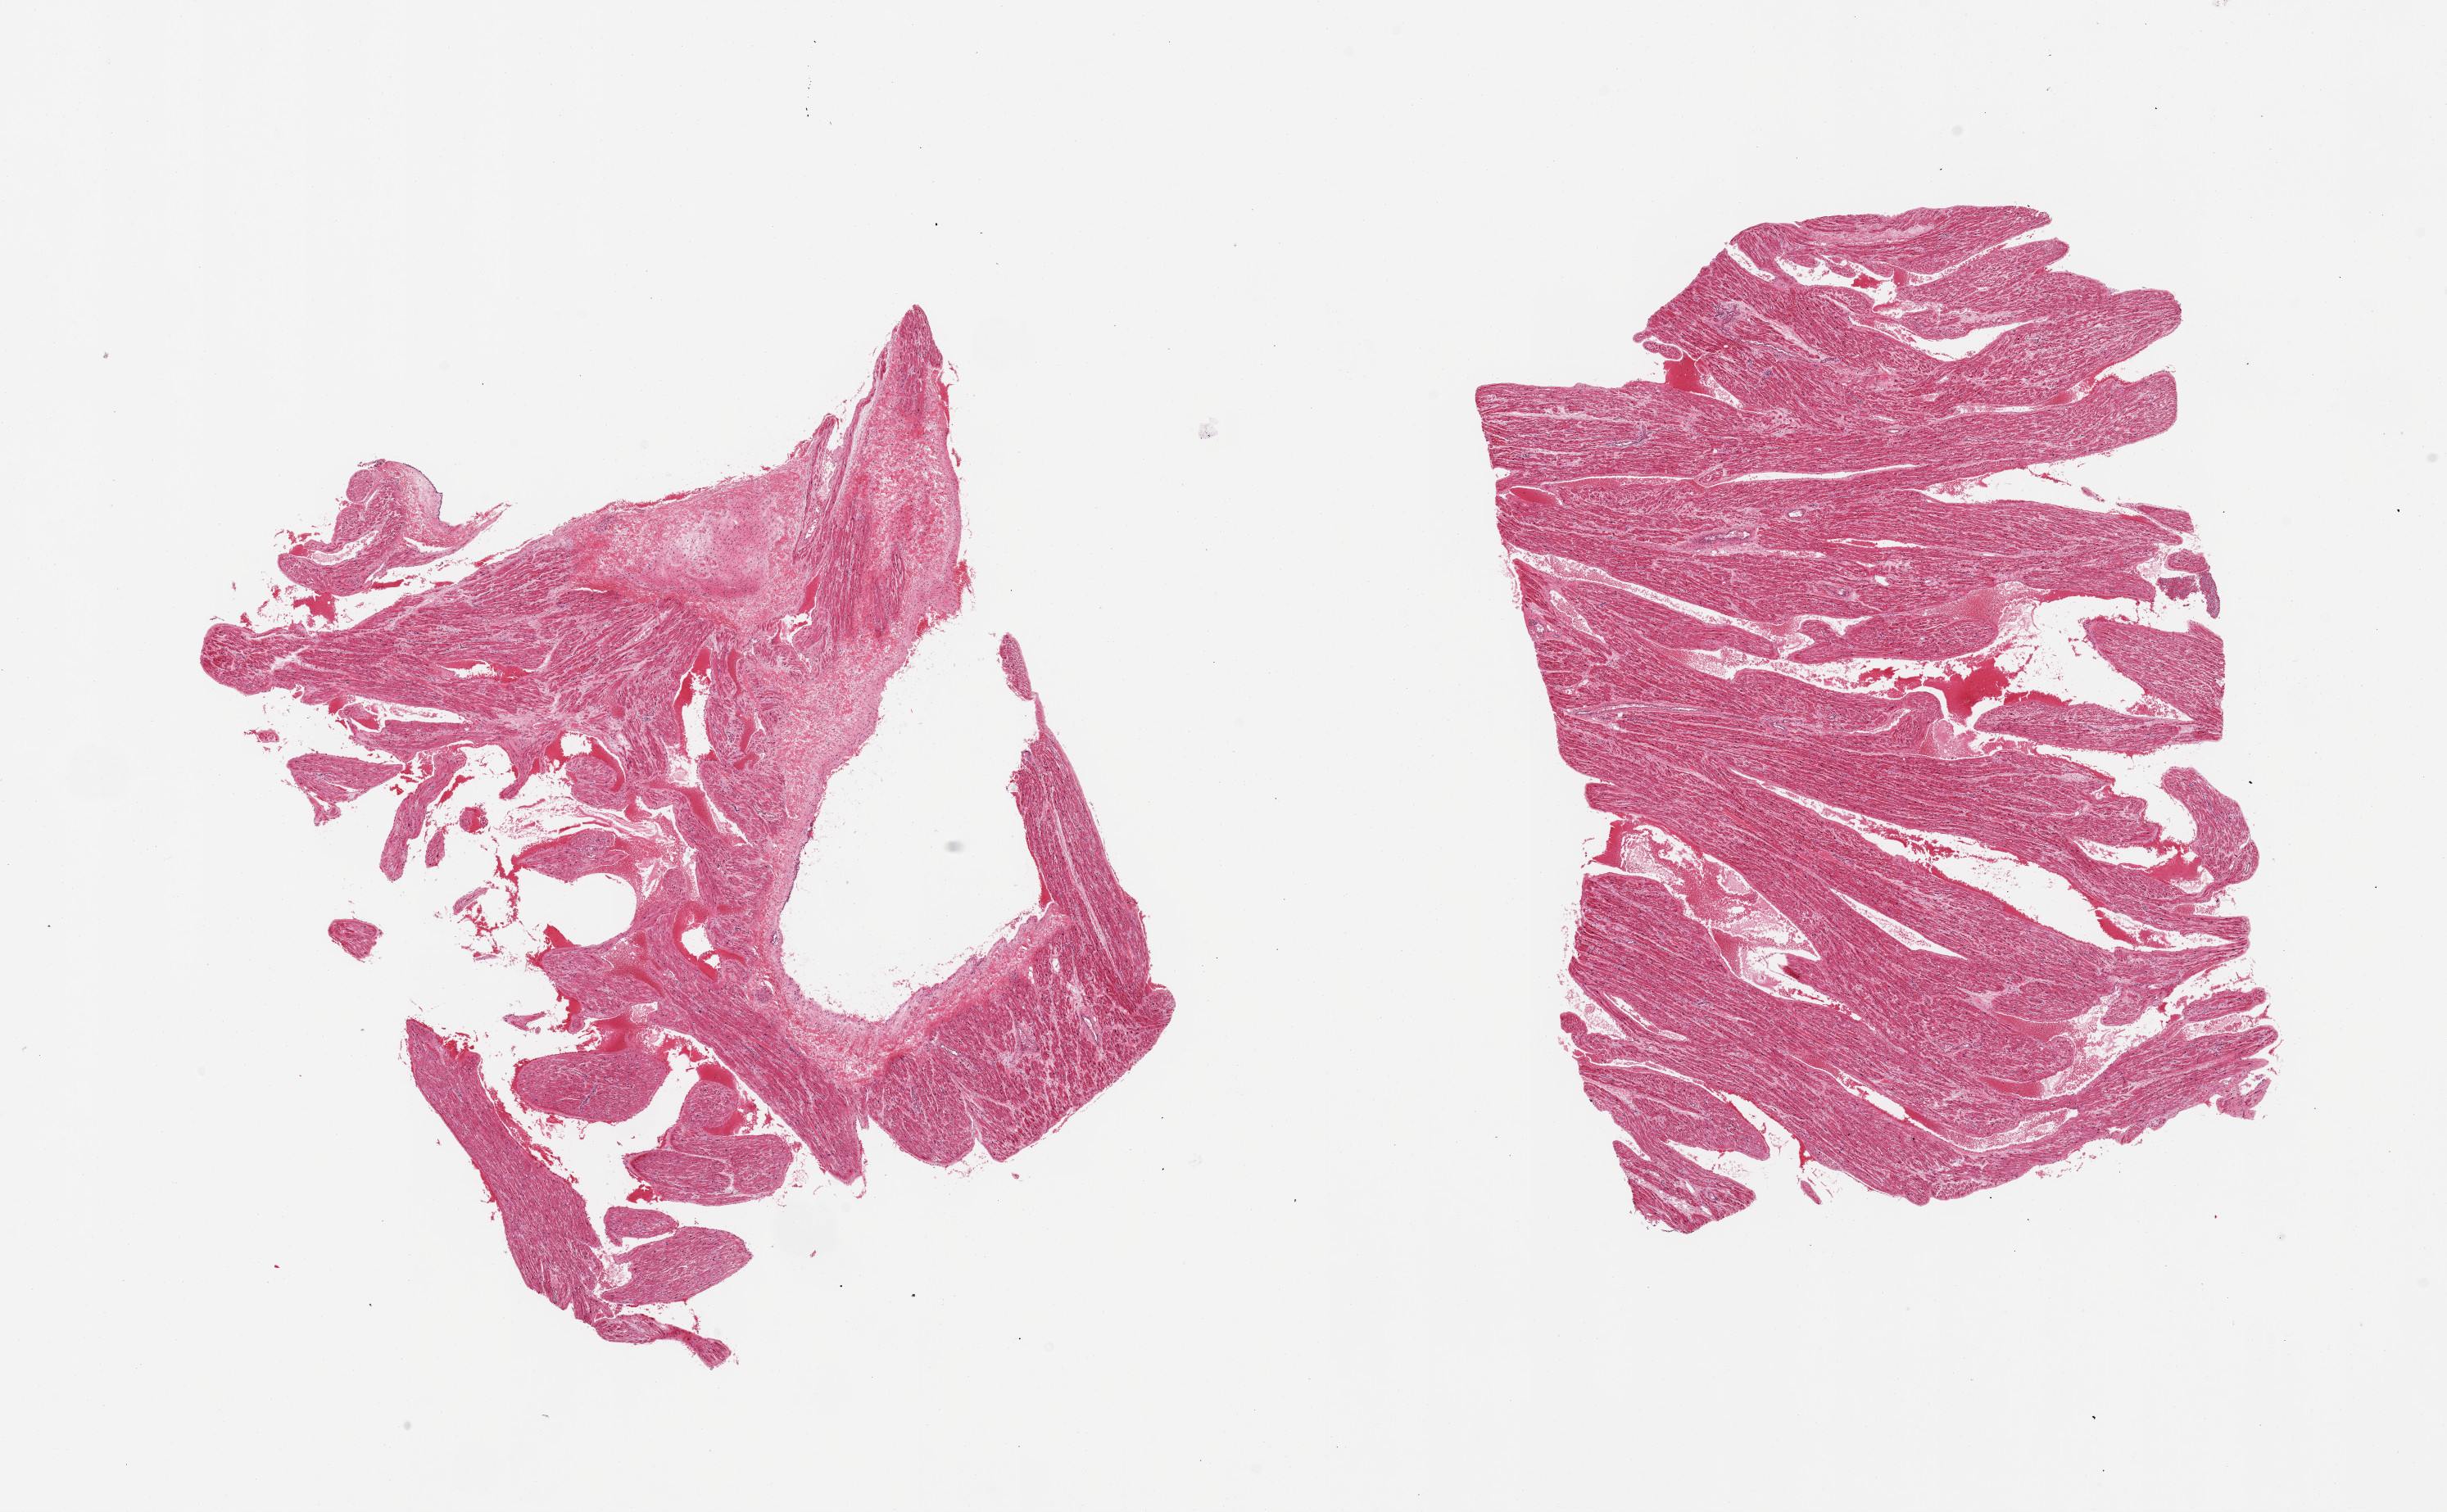
Digitized H&E-stained section, whole scanned area (about 23.6 x 14.6 mm) shown as a low-resolution overview; PAXgene-fixed, paraffin-embedded tissue; target tissue: auricular appendage; tissue donor sample. Donor sex: male.
• reviewer comment on this tissue sample: 2 pieces; ~20% of one is fibrous, small contaminating fragment of spleen